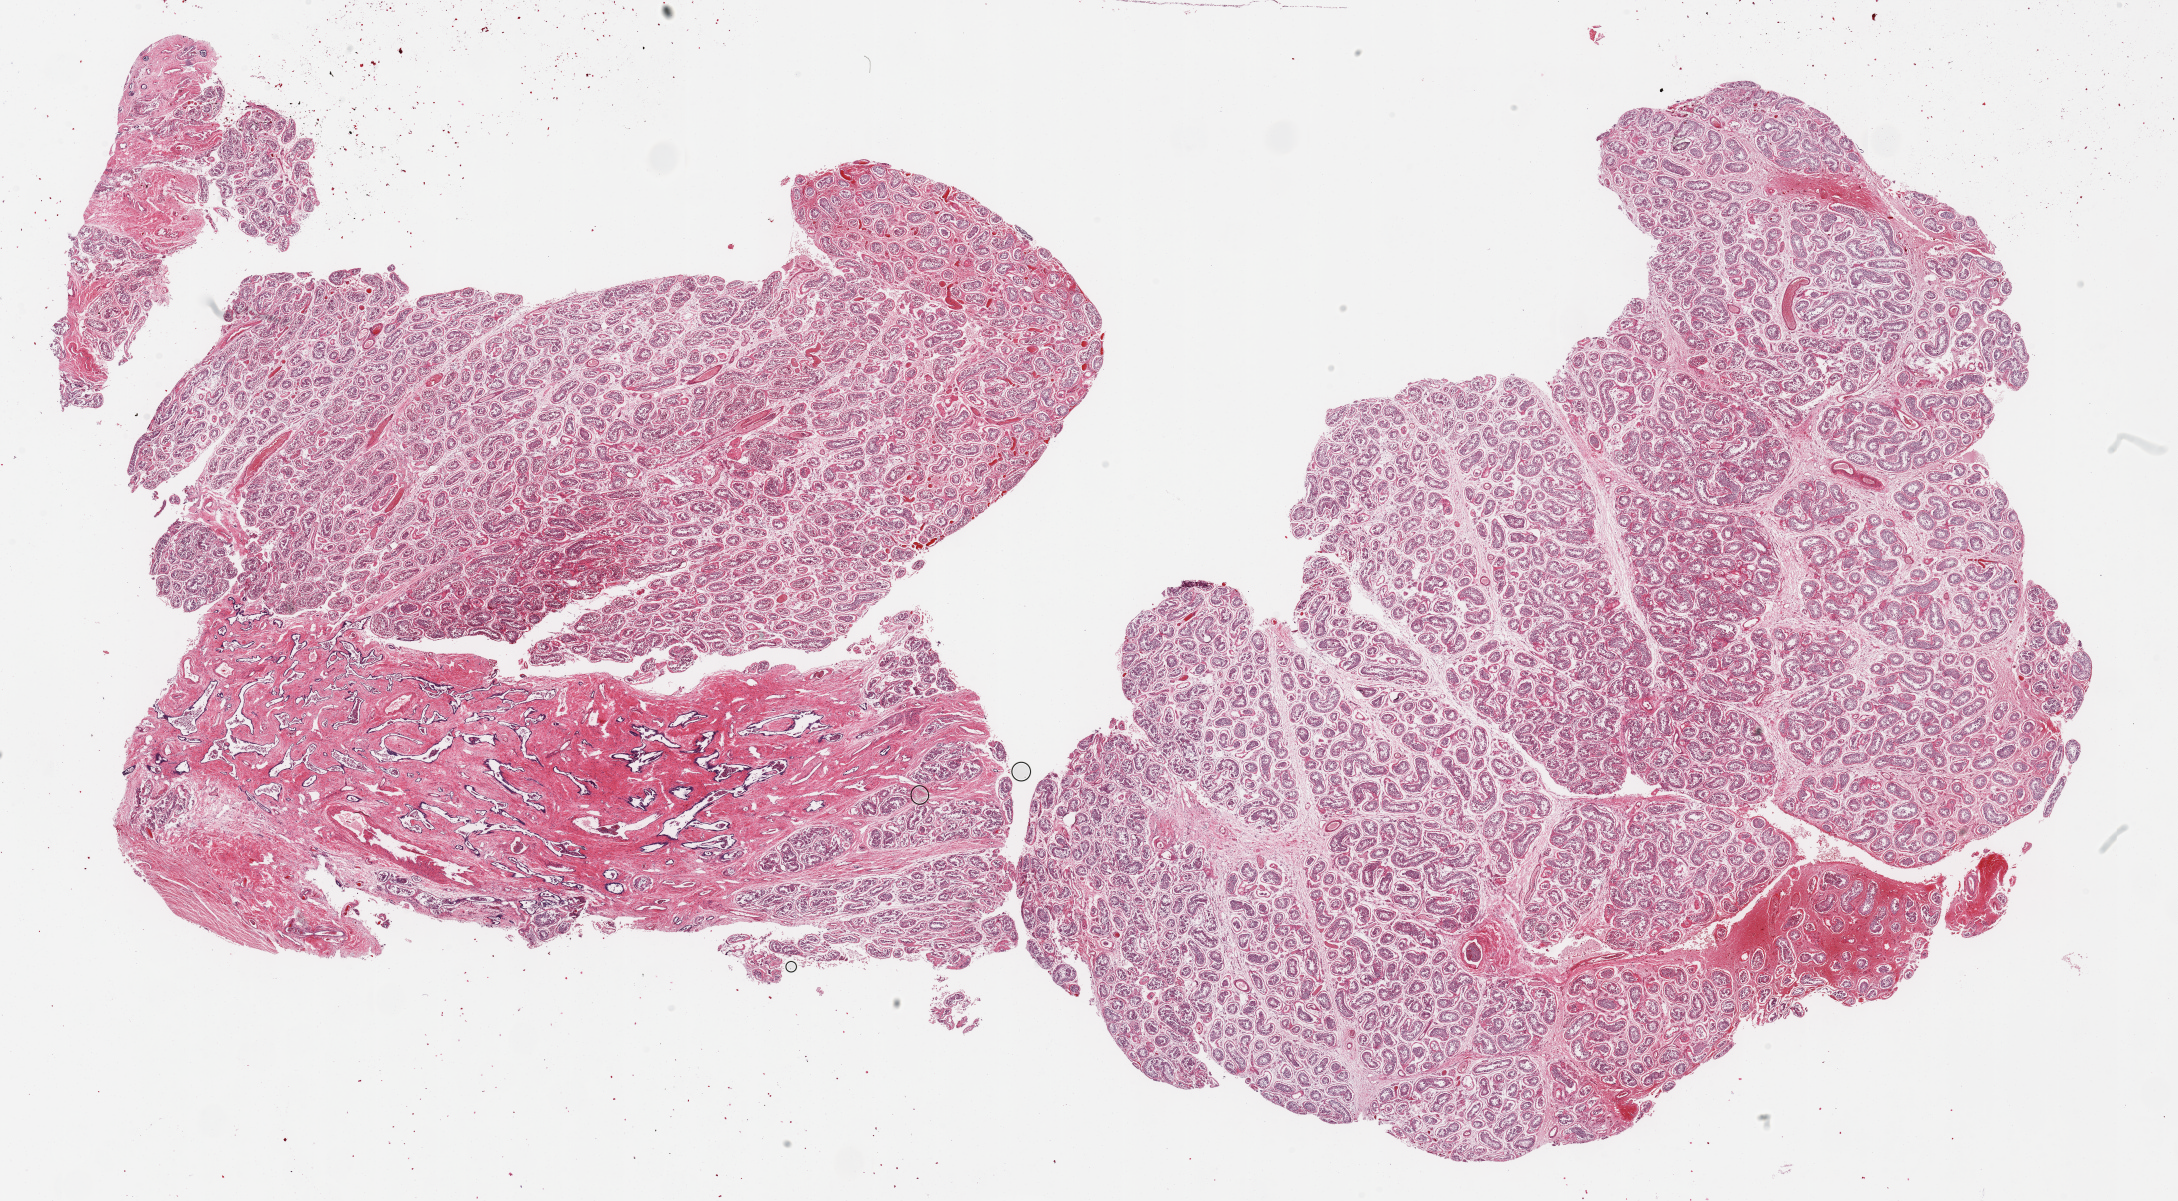
Digitized haematoxylin and eosin-stained section — whole scanned area (about 34.5 x 19.0 mm) shown as a low-resolution overview; PAXgene-fixed paraffin-embedded (PFPE) section; target tissue: testis; tissue donor sample. Donor: male.
Pathologist's review note for this sample: 2 pieces; moderately advanced autolysis; spermatogenesis appears reduced.